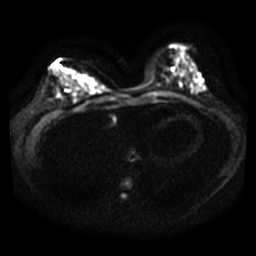
Breast MRI, one axial slice. Position 14 of 40 along the scan axis. Diffusion-weighted series; image 2 of 4 stored at this slice position (different b-values; order by instance number). 3 T. 5 mm slice thickness. 256 × 256 image matrix, field of view 340 × 340 mm. Female patient.
Annotated regions visible in this slice (expert manual segmentation):
- tumour on diffusion-weighted imaging: bounding box [x1, y1, x2, y2] px = [78, 77, 96, 90]